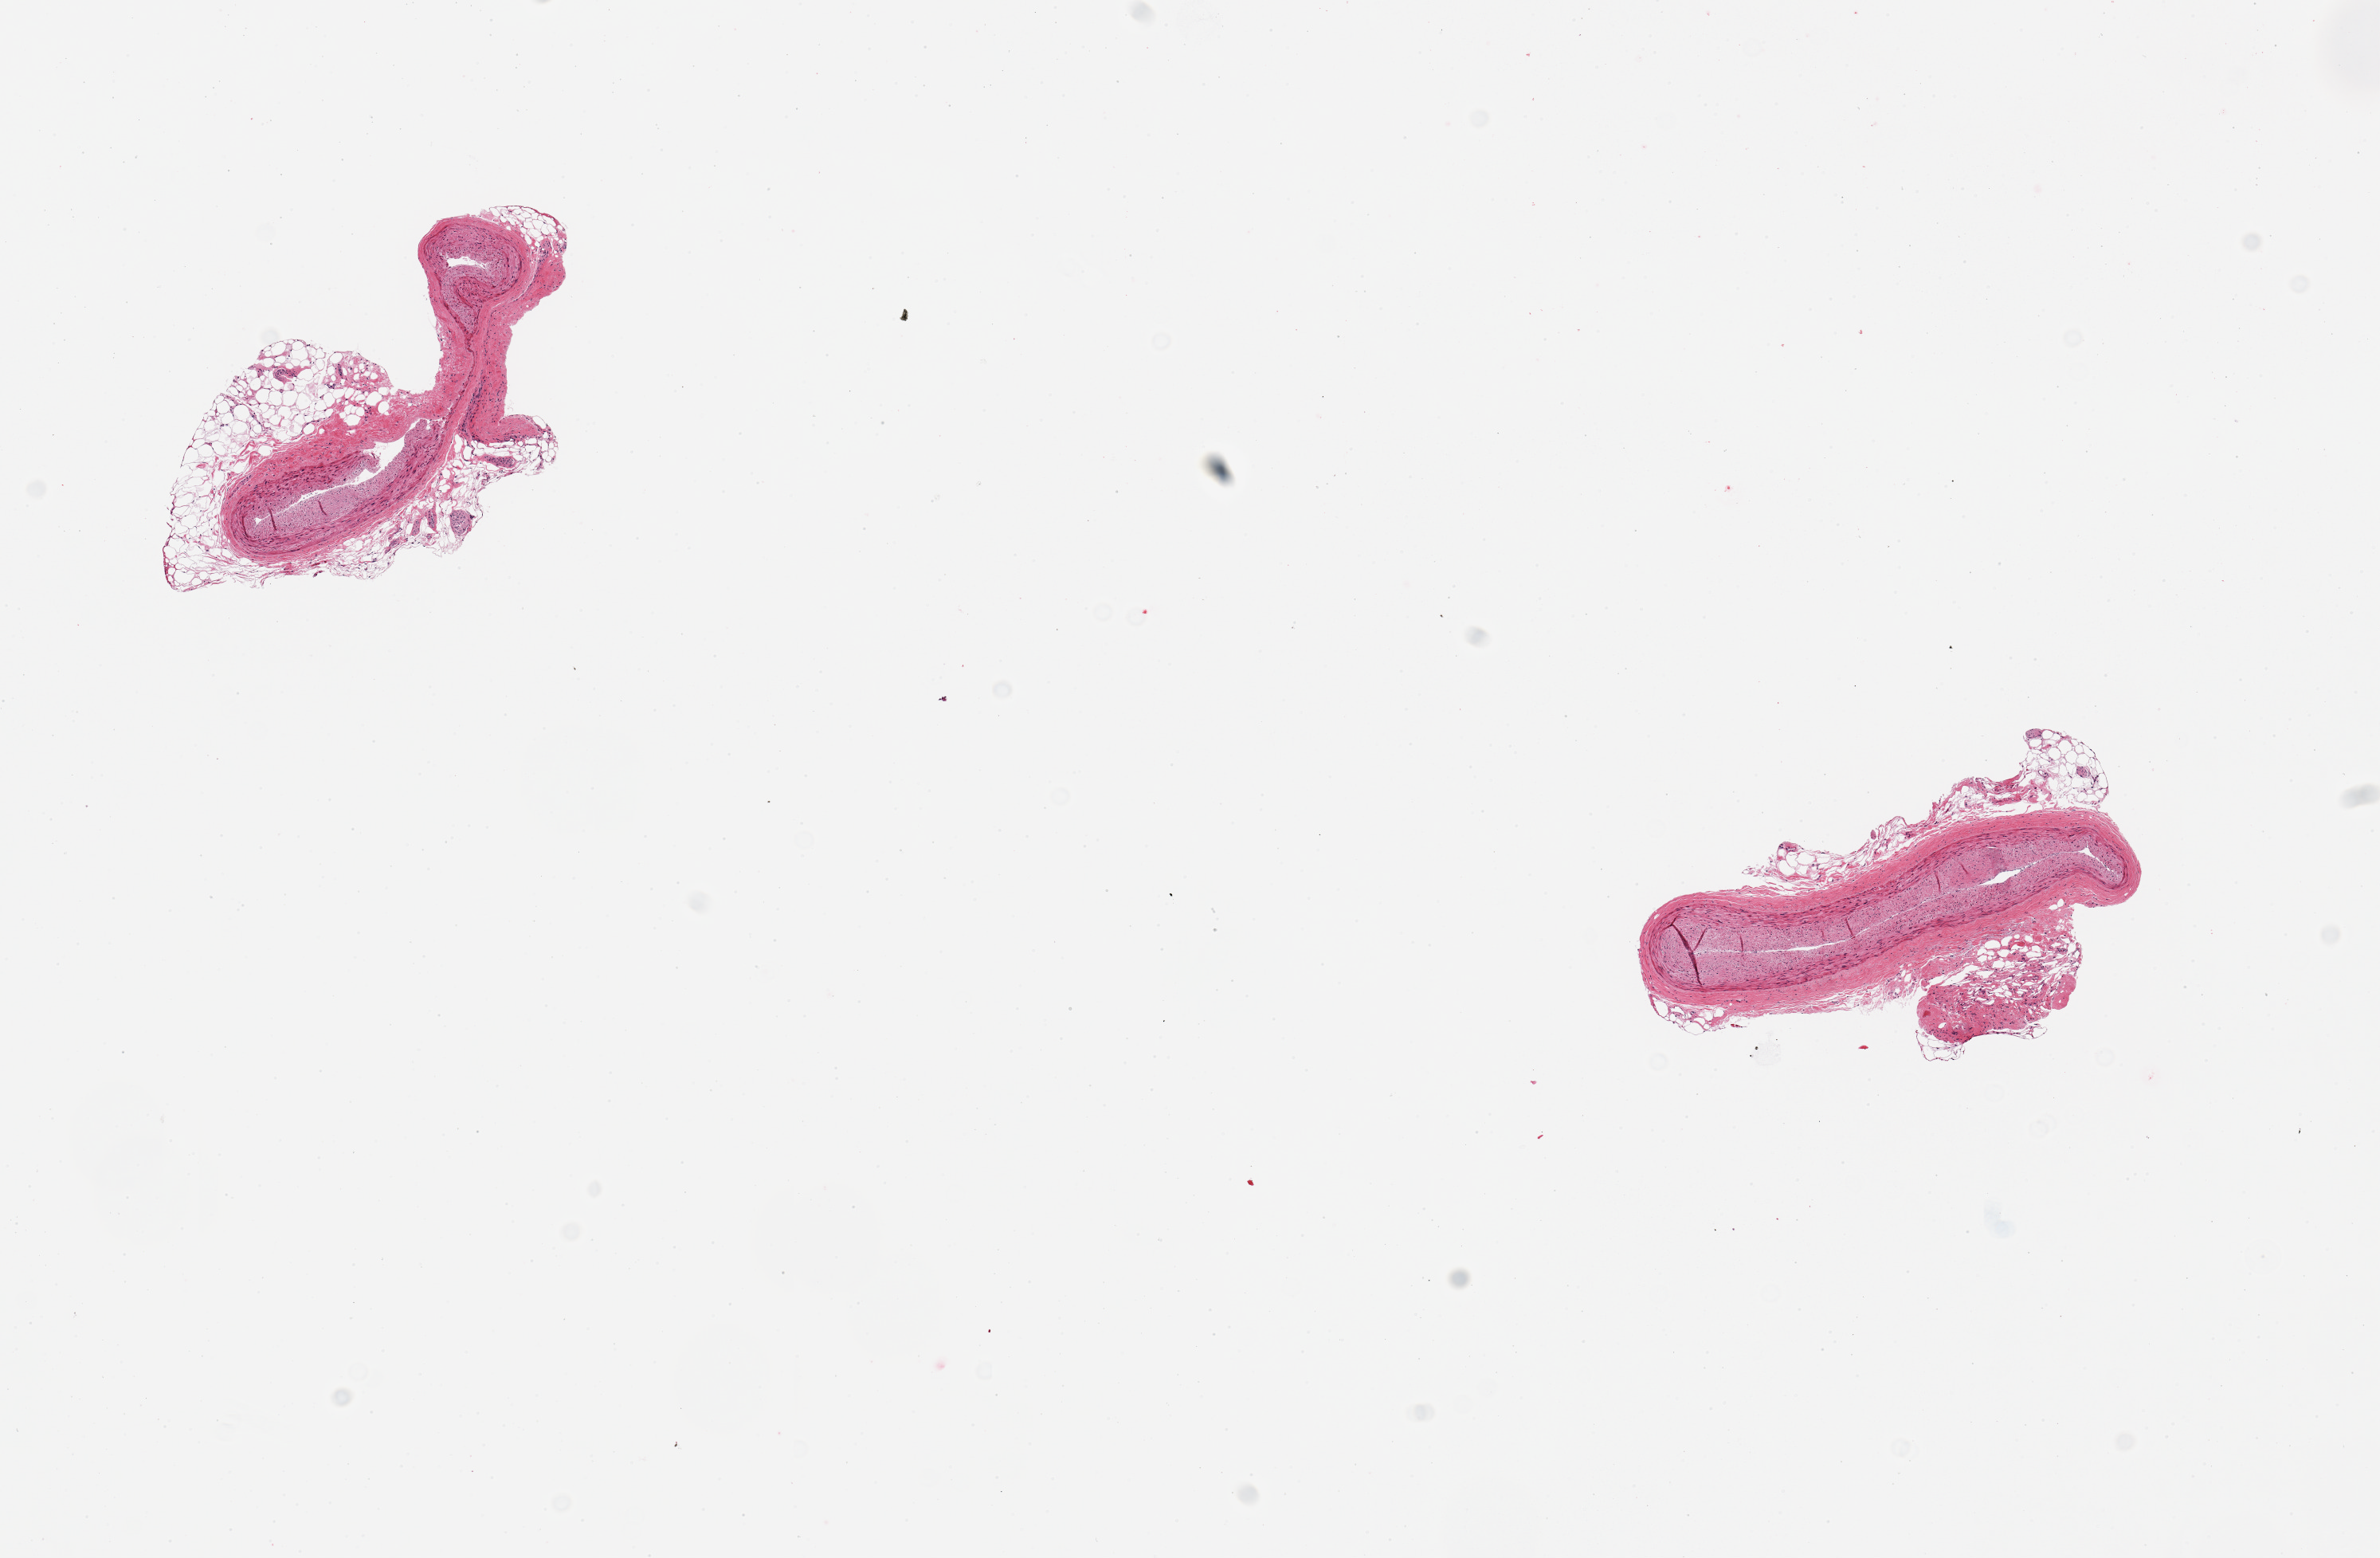
Digitized hematoxylin and eosin (H&E)-stained section, a low-resolution overview of the entire scanned area, about 11.8 x 7.7 mm, PAXgene-fixed paraffin-embedded (PFPE) section, sampled site (target tissue): coronary artery, donor tissue sample. Donor sex: male.
• reviewer comment on this tissue sample: 2 pieces adherent rims of fat up to ~1.5mm; No atherosis